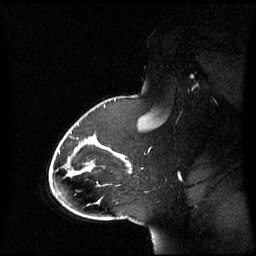
Breast MRI (dynamic contrast-enhanced), one sagittal slice; slice 44 of 60 in the series (ordered by position); dynamic contrast-enhanced series, image 2 of 3 at this slice position (ordered by acquisition); 1.5 T; TE 4.2 ms, TR 8.4 ms; 256 × 256 image matrix. Female patient, age 43 years. Case-level facts recorded for this patient, not image findings: setting: breast cancer imaged before/during neoadjuvant chemotherapy; receptor status: triple-negative.
Structures marked on this image (semi-automatically segmented with operator editing):
- analysis volume of interest (the breast-tissue region the enhancement analysis was run in; not a lesion): bounding box <65,118,143,198> (left, top, right, bottom; pixels)
- tumour enhancement mask (voxels above the 70 % enhancement threshold inside the analysis volume of interest): <95,144,131,166>